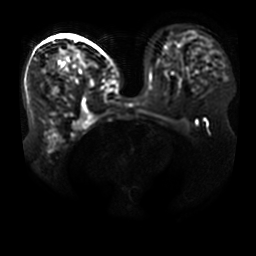
Breast MRI, one axial slice; slice 24 of 41 in the series (ordered by position); diffusion-weighted series; image 2 of 4 stored at this slice position (different b-values; order by instance number); 3 T; 5 mm slice thickness; 256 × 256 image matrix, field of view 400 × 400 mm. Female patient.
Outlined on this slice (outlined manually by an expert reader):
- tumour on diffusion-weighted imaging: box from (x=51, y=49) to (x=96, y=86) px